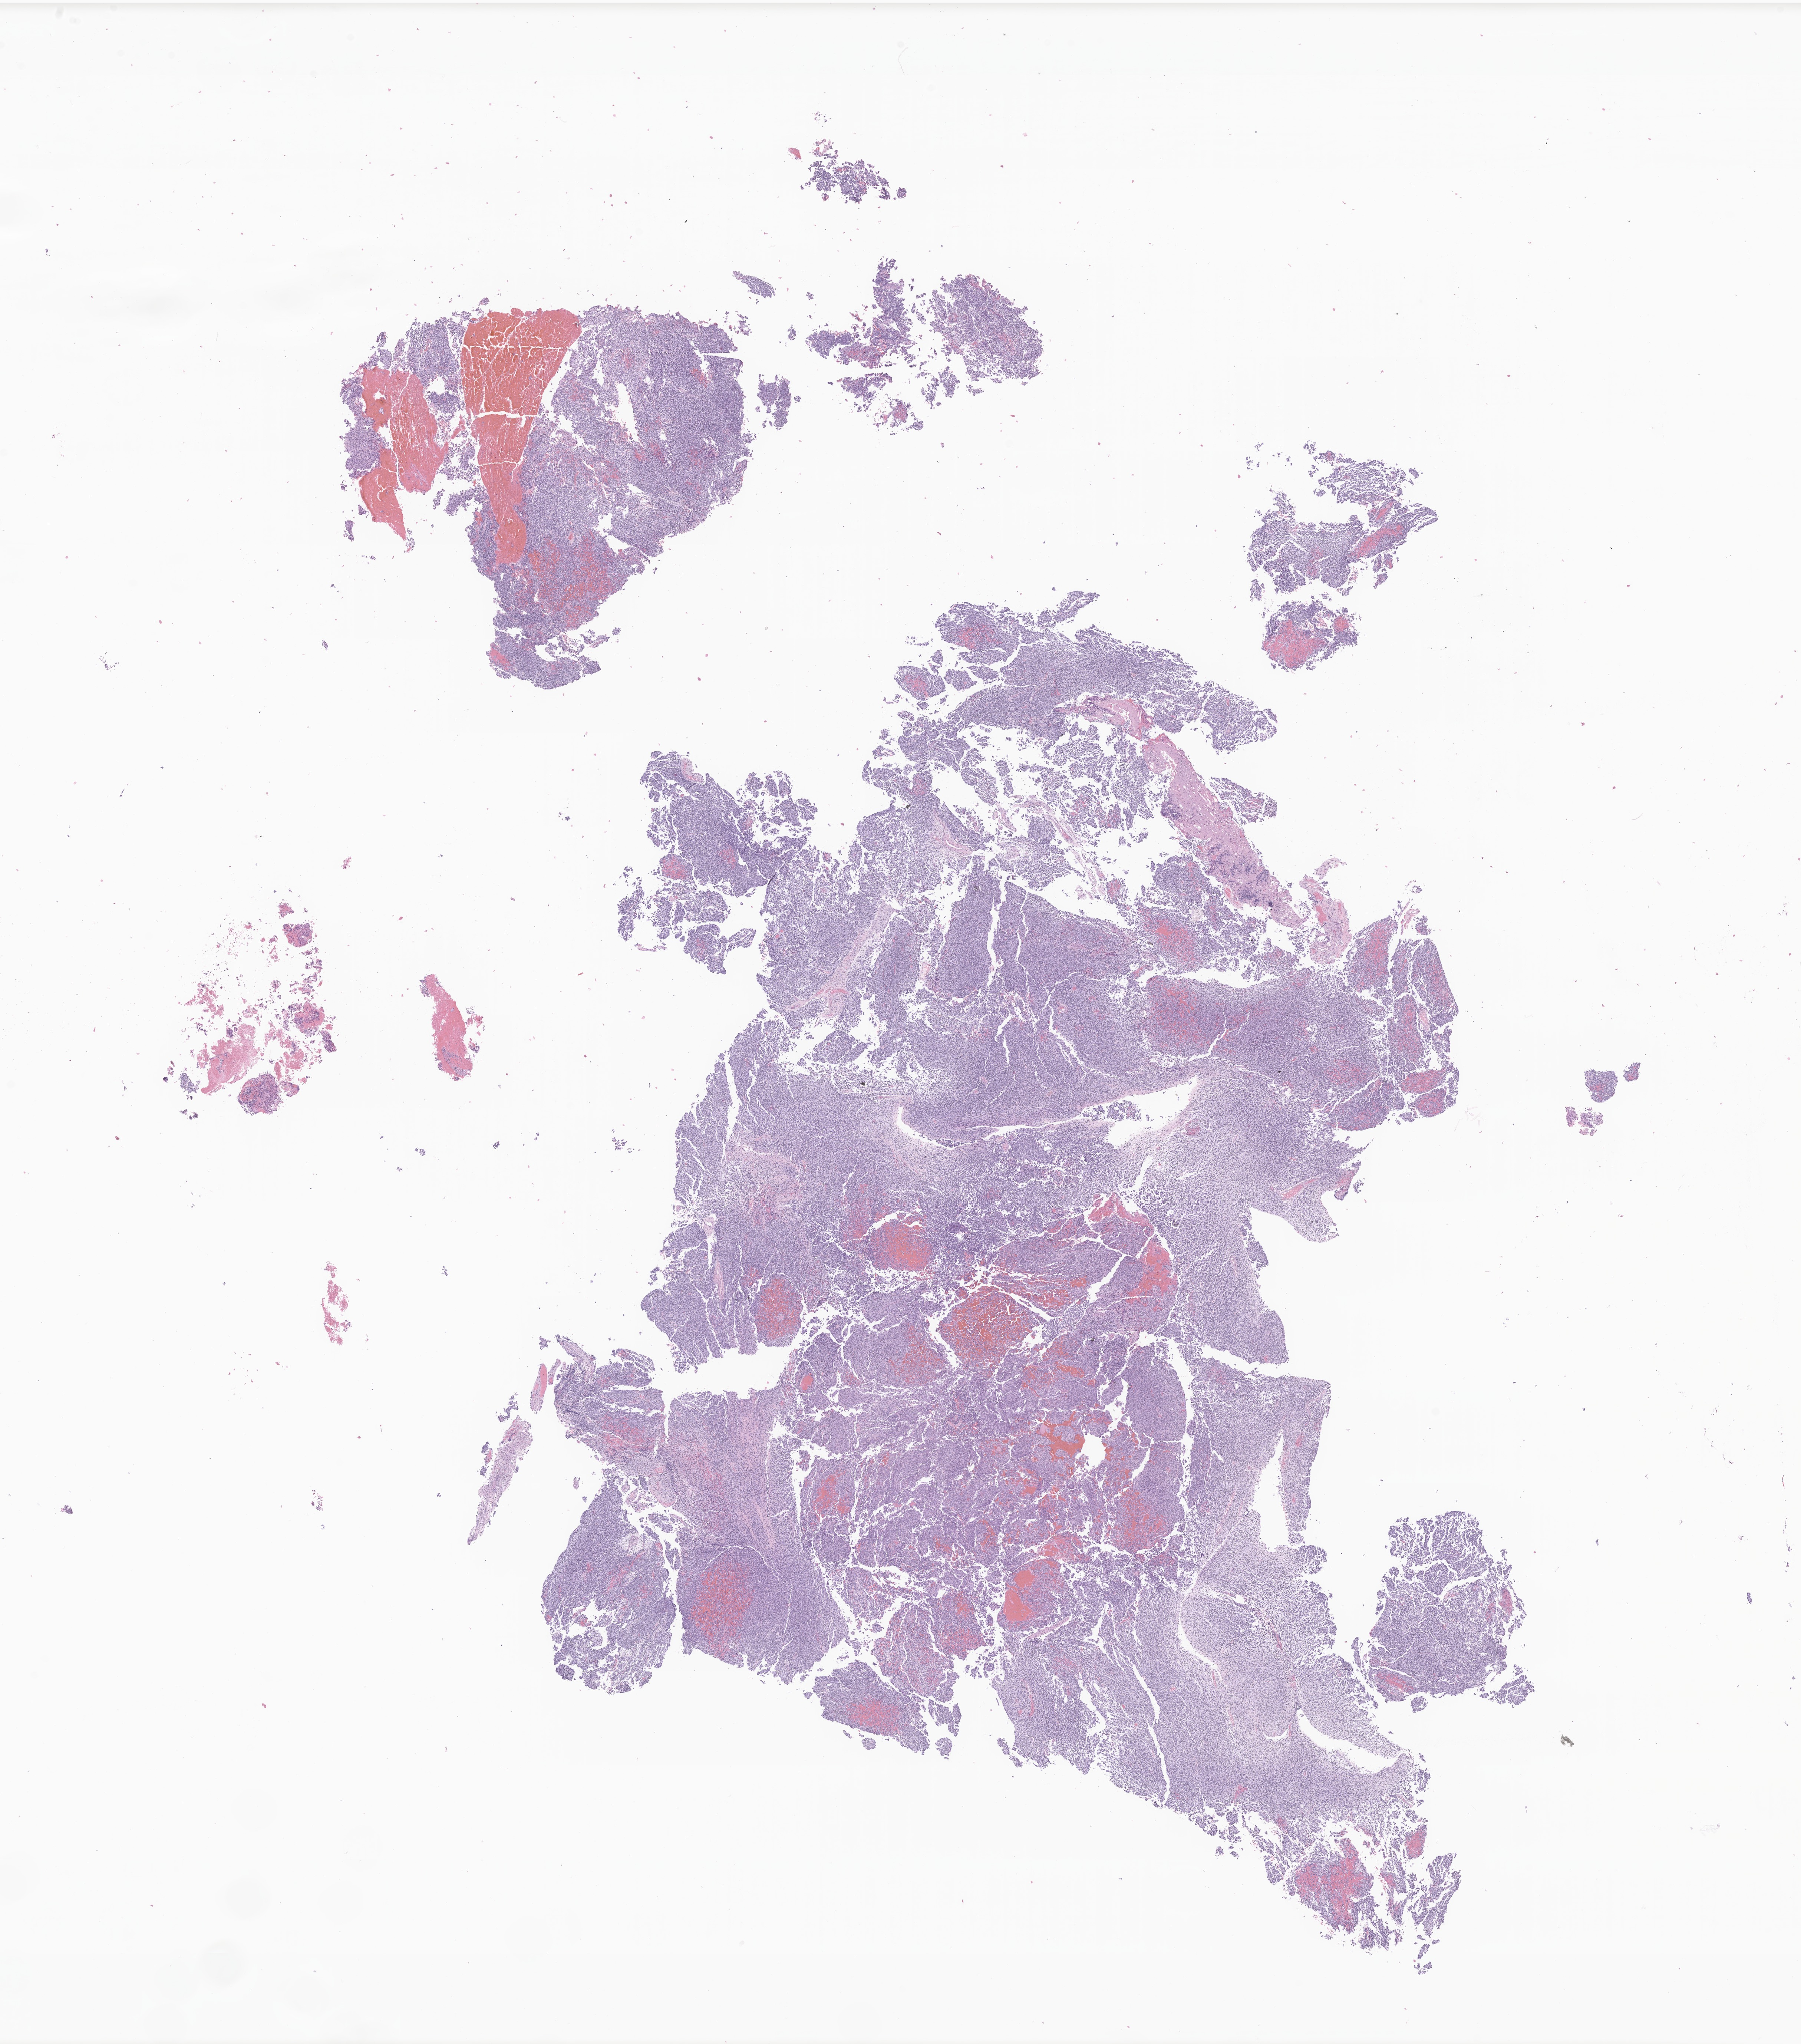
Whole-slide image, H&E stain of tumor tissue from the brain — a low-resolution overview of the entire scanned area, about 20.5 x 23.2 mm; FFPE section. Patient male; age 45 months (3 years 9 months).
* recorded diagnosis: Medulloblastoma, NOS